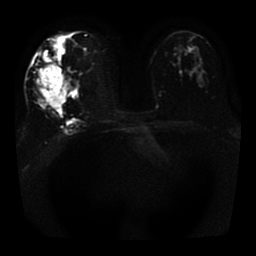
Breast MRI, one axial slice; position 21 of 41 along the scan axis; diffusion-weighted series; image 2 of 4 stored at this slice position (different b-values; order by instance number); 1.5 T; 5 mm slice thickness; 256 × 256 image matrix, field of view 330 × 330 mm. Female patient.
Structures marked on this image (expert manual segmentation):
- tumour on diffusion-weighted imaging: bounding box <39,56,66,109> (left, top, right, bottom; pixels)